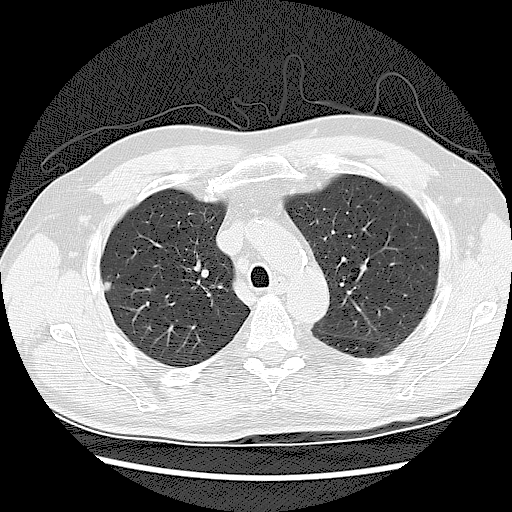
Chest CT (low-dose screening protocol), one axial image, second annual screen, lung window (W 1500 / L -600 HU), 2.5 mm slice thickness, 512 × 512 image matrix. Male, age 62 years at enrolment. Former smoker at enrolment.
• Expert-annotated lung lesion, bounding box <92,273,122,299> (left, top, right, bottom; pixels).
• Reader record for this screening exam (exam-level; its link to the box is not recorded): non-calcified nodule or mass ≥4 mm, right upper lobe, 10 × 10 mm, smooth margins, soft tissue attenuation, pre-existing on the prior screen: yes; interval growth: yes.
• Official screen result: positive, other.
• Later outcome: lung cancer diagnosed 6 days after this screen — adenocarcinoma, NOS, right upper lobe, poorly differentiated (G3), stage IIB (AJCC 6th edition), 5 mm at pathology.